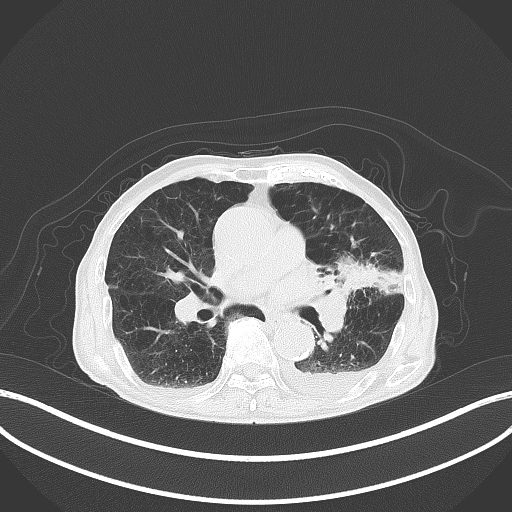
Chest CT, one axial slice. Position 189 of 227 along the scan axis. Reconstruction kernel B70f. Lung window (W 1500 / L -600 HU). 3 mm slice thickness. 512 × 512 image matrix, field of view 400 × 400 mm. Patient: male, 90 years or older. From the clinical record (not read from this slice): clinical TNM (as recorded): T2b N1 M0.
Structures marked on this image (rectangle marked by the reading radiologist):
- lung tumour (recorded histology: squamous cell carcinoma): box from (x=333, y=254) to (x=398, y=296) px